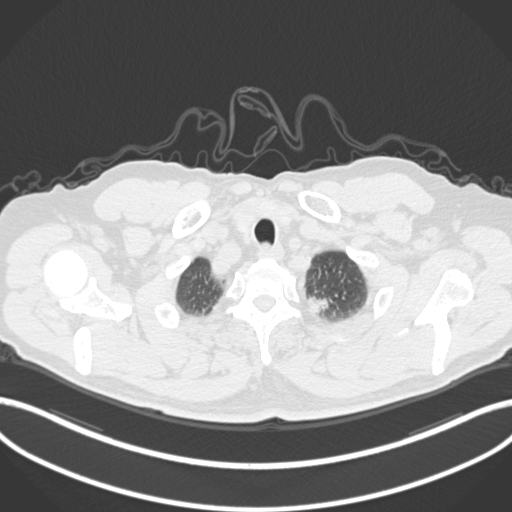
Chest CT, one axial slice; position 295 of 306 along the scan axis; reconstruction kernel B30f; 120 kVp; lung window (W 1500 / L -600 HU); 1 mm slice thickness; 512 × 512 image matrix, field of view 400 × 400 mm. Patient: male, 64 years. Case-level facts recorded for this patient, not image findings: clinical TNM (as recorded): T1c N0 M0.
Outlined on this slice (bounding box drawn by a radiologist):
- lung tumour (recorded histology: adenocarcinoma): bounding box (x1, y1, x2, y2) in pixels: (306, 289, 333, 316)